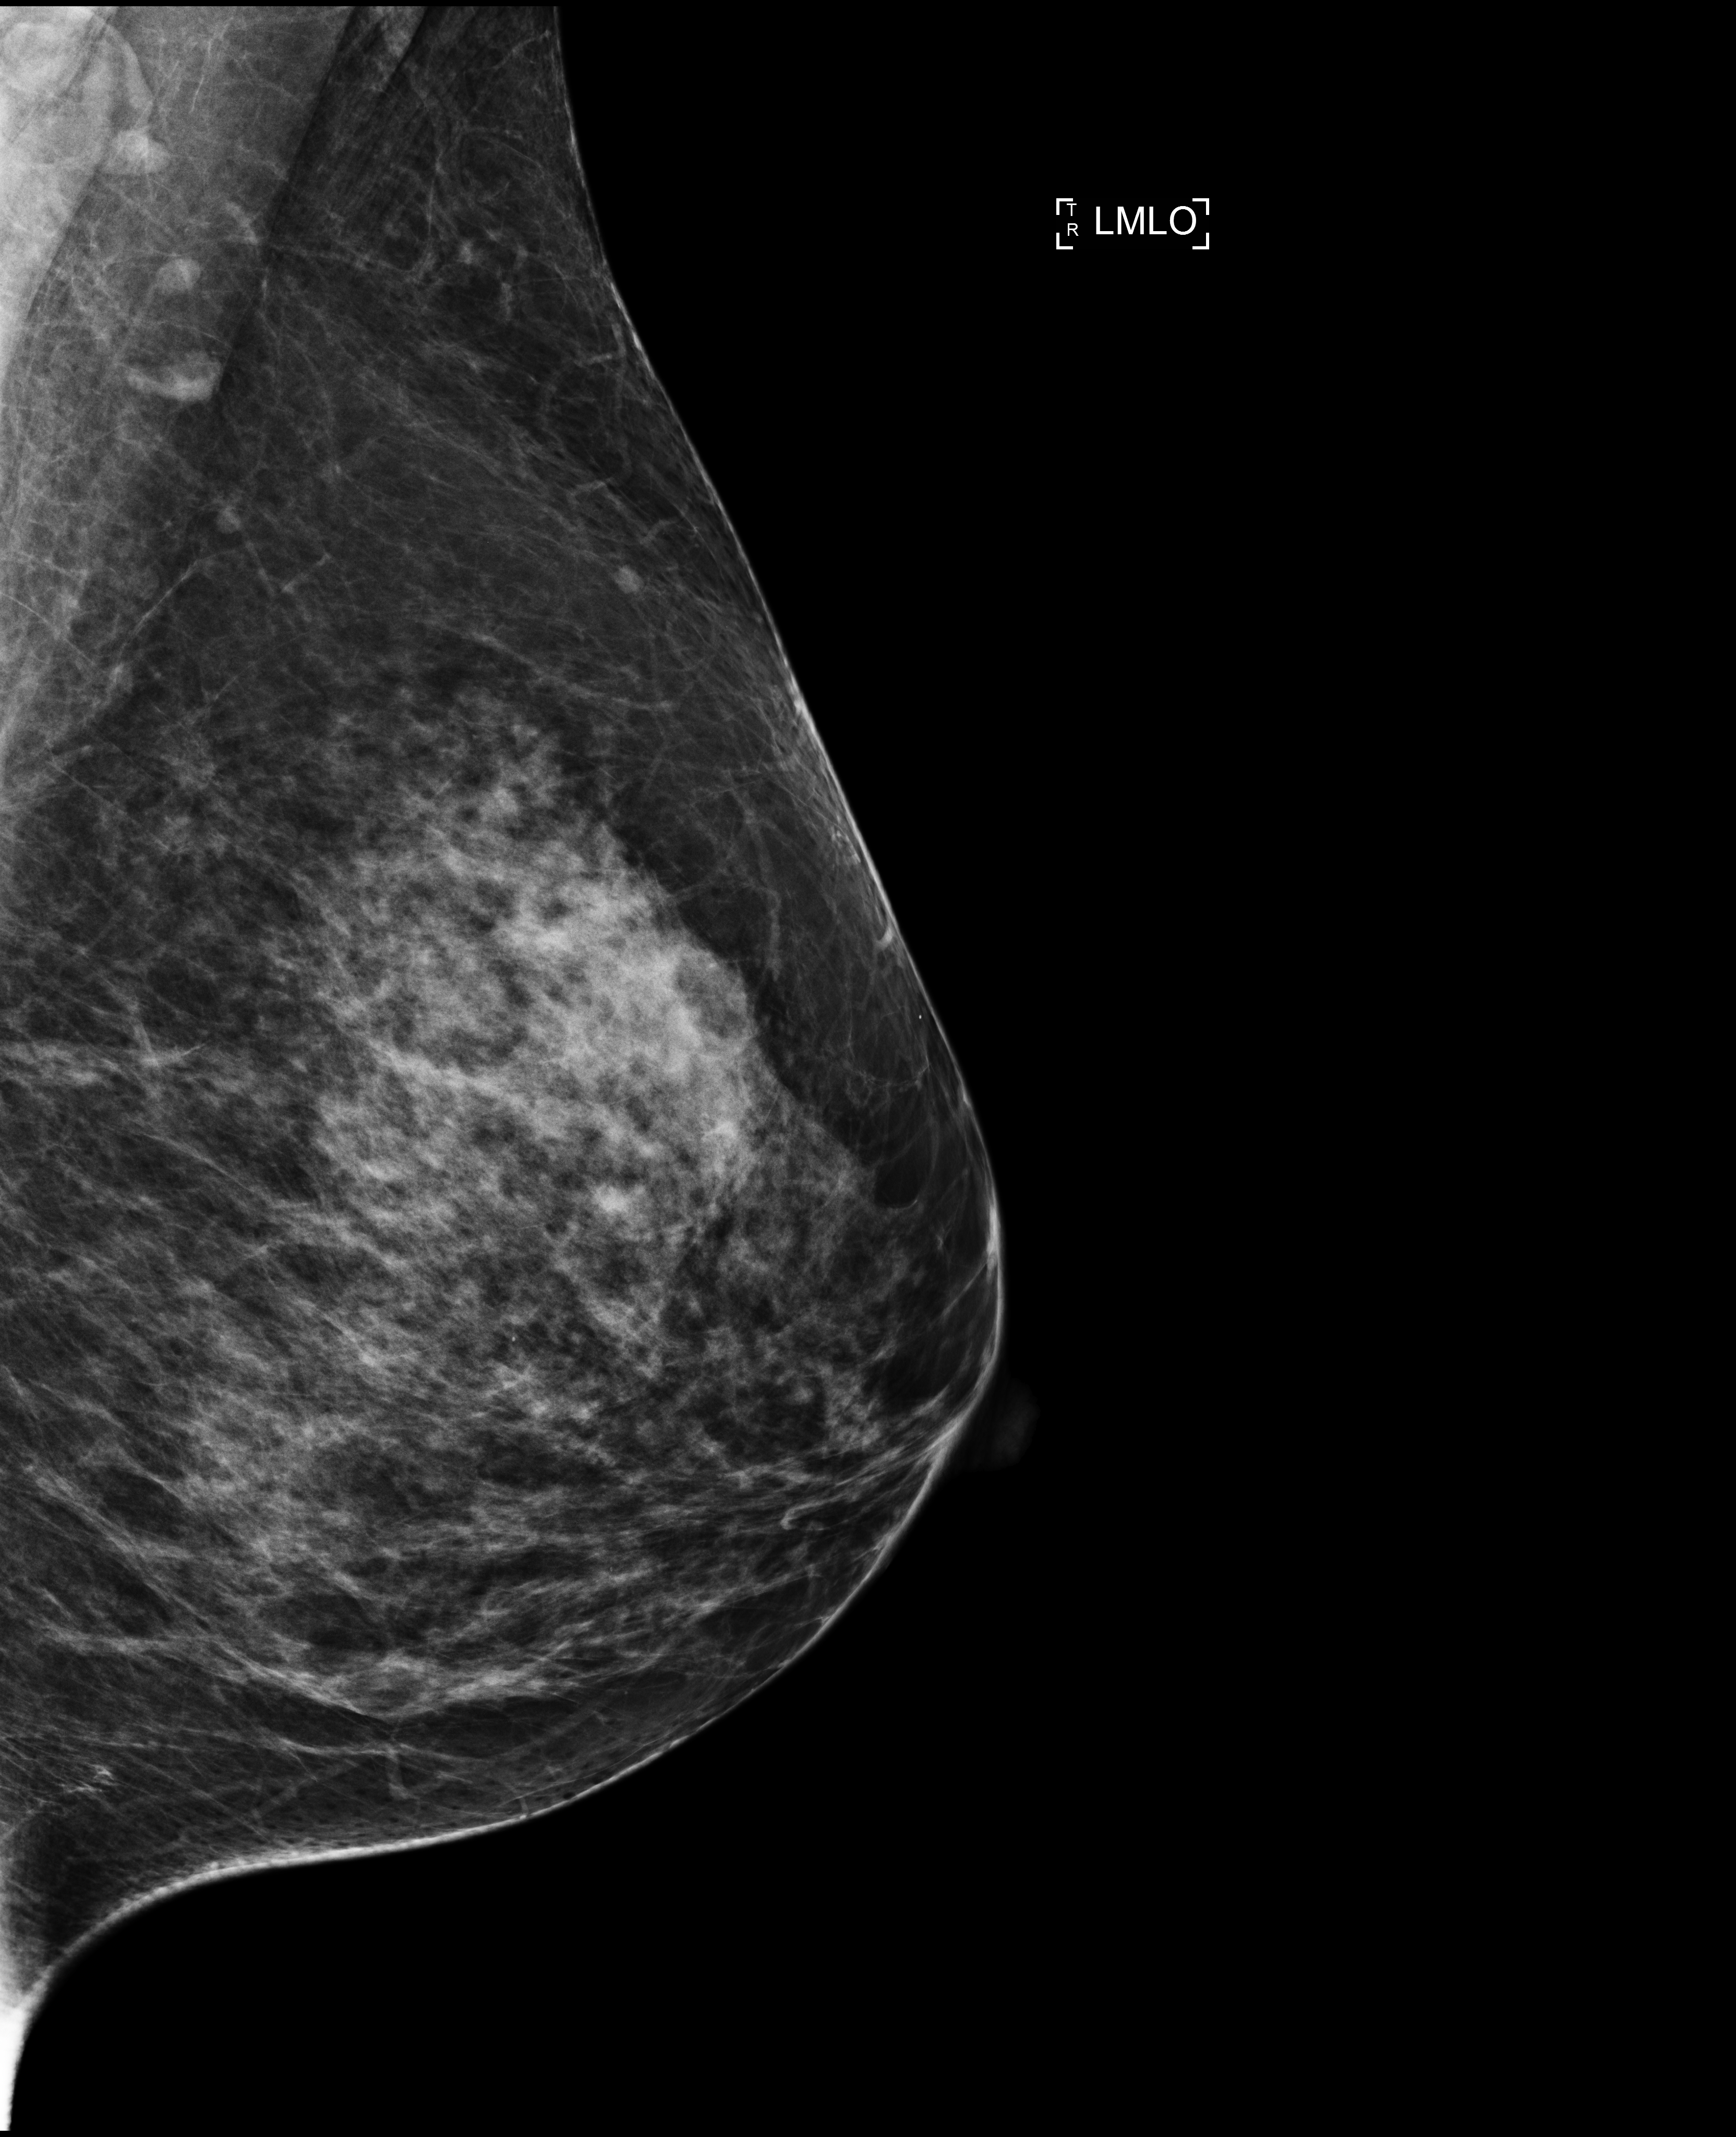
Full-field digital mammogram (FFDM), left breast, mediolateral oblique (MLO) view, screening examination, compressed breast thickness 80 mm. Female patient, age 46 years.
- breast density at the screening exam (both breasts): heterogeneously dense (BI-RADS density category c)
- final BI-RADS category for the screening round (tomosynthesis exam, both breasts): category 1
- recall: no recall after this screen